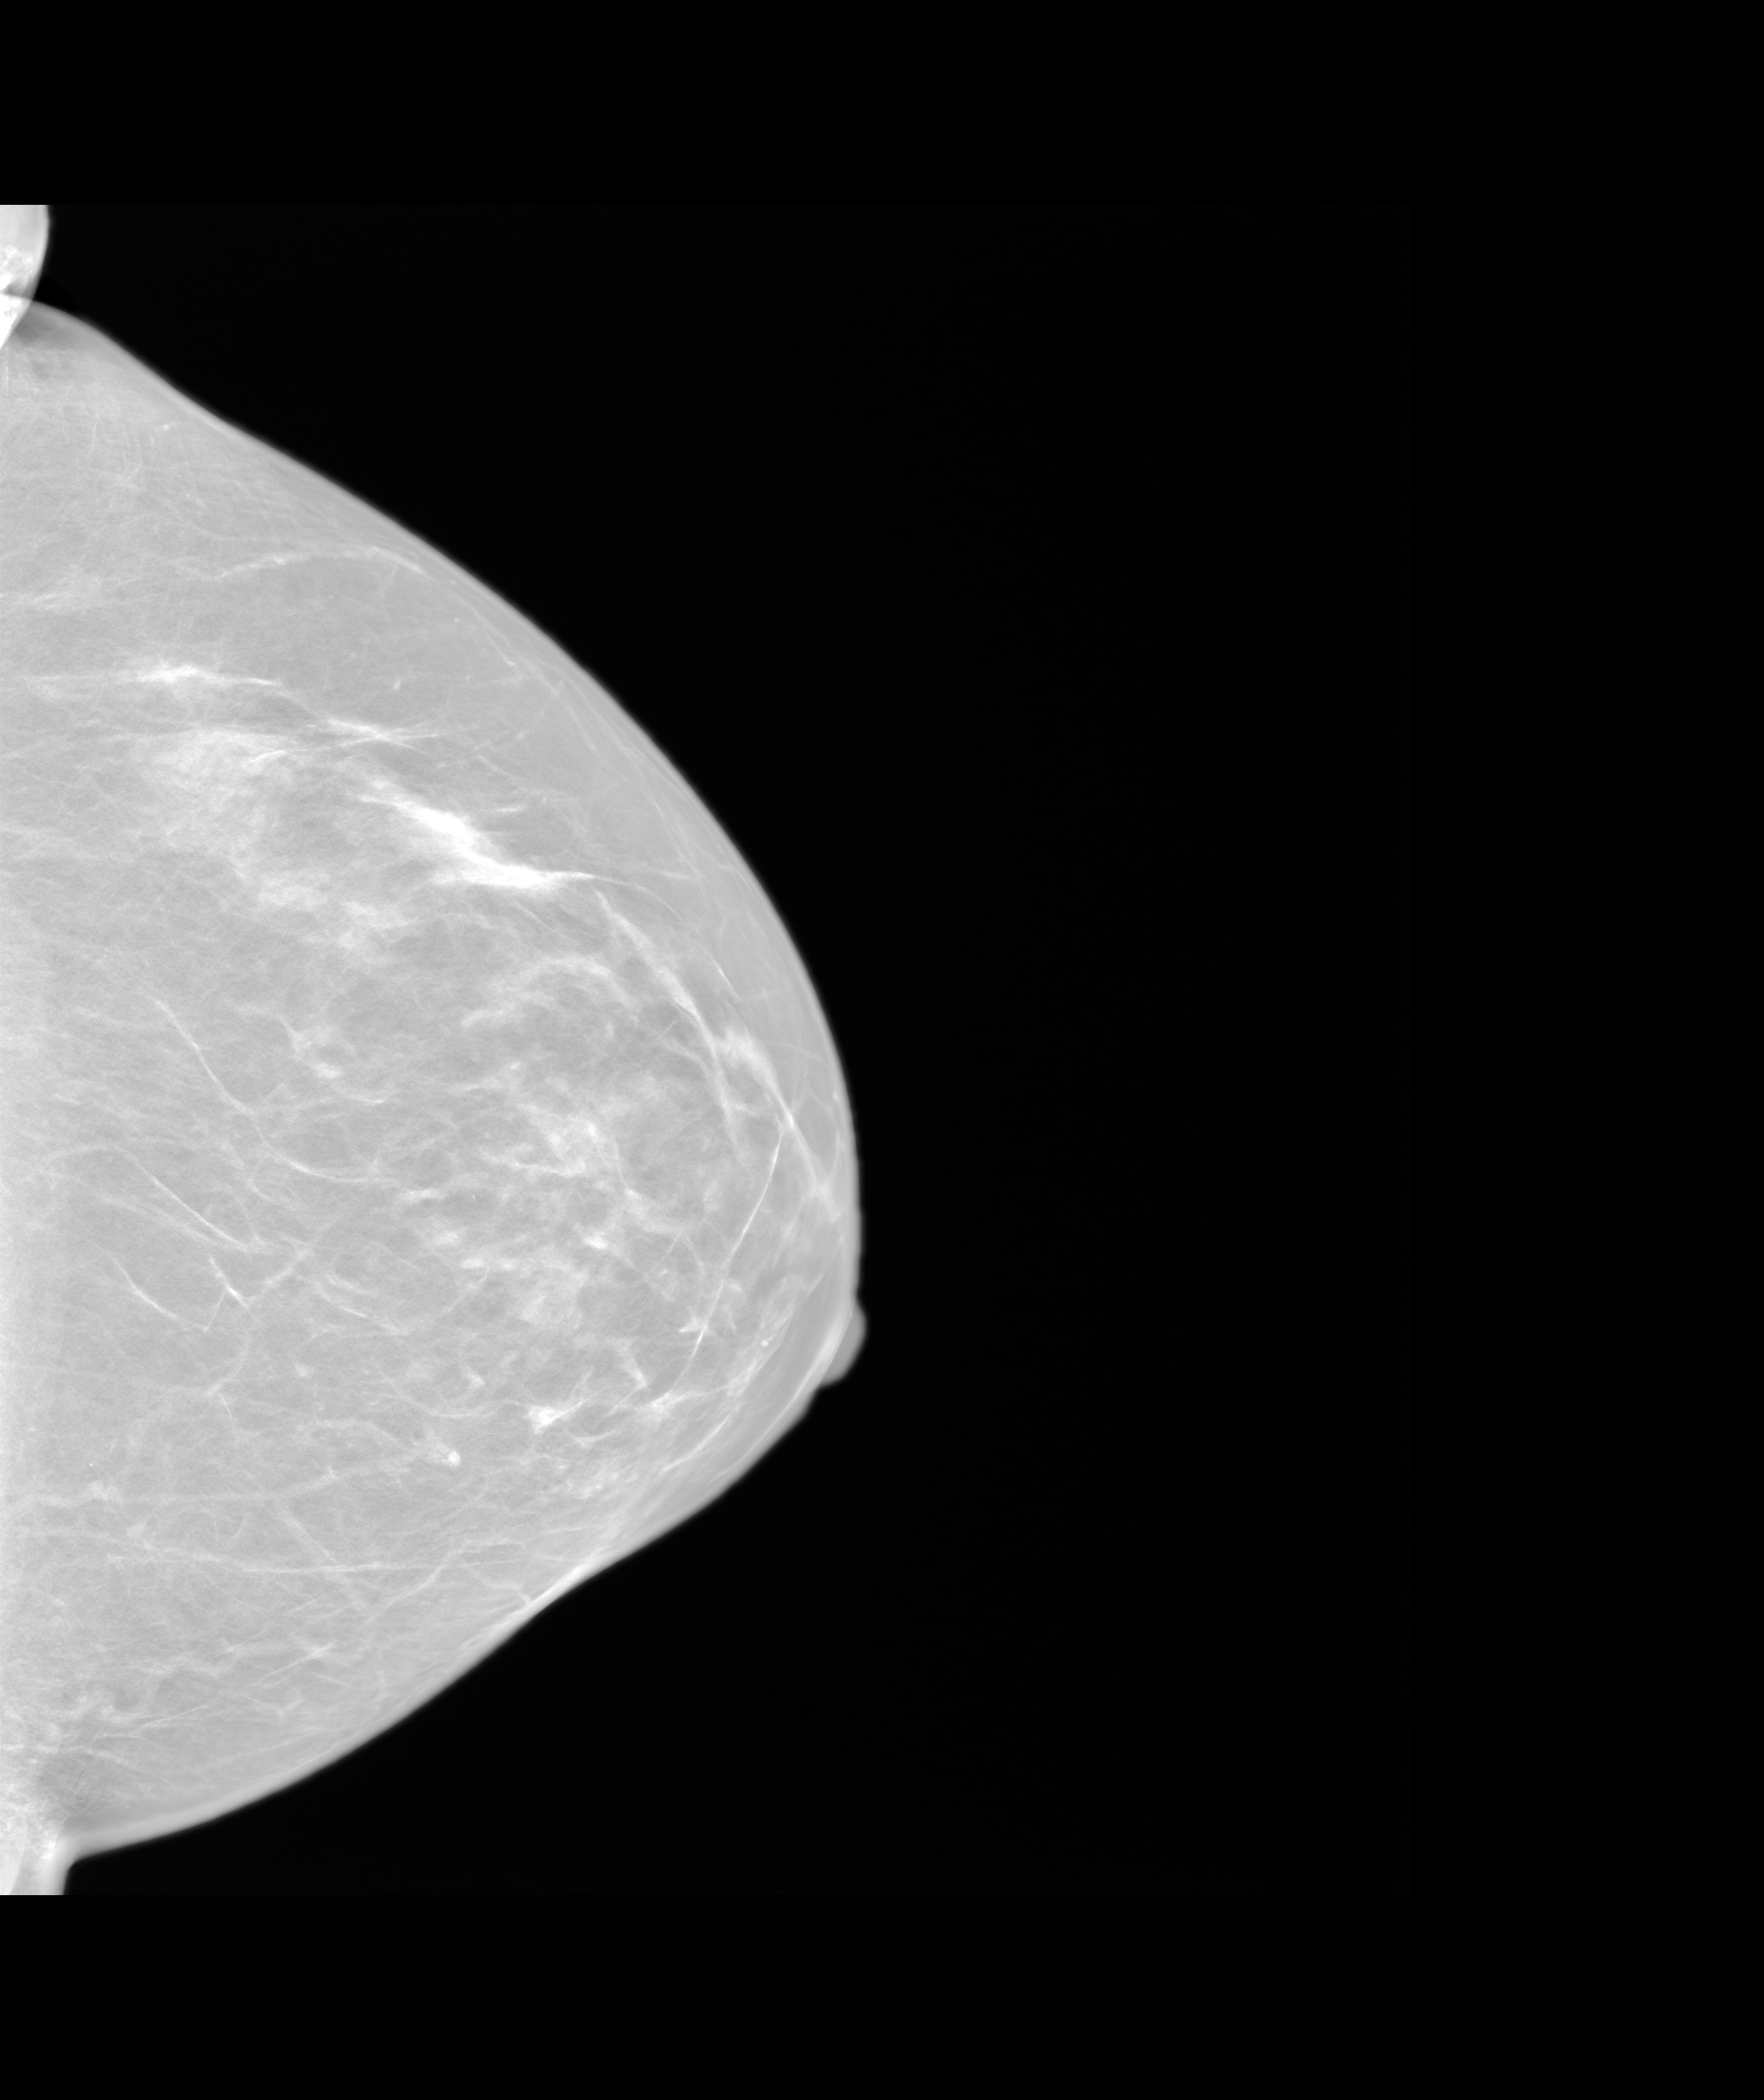
Annual screening mammography examination, system: SenoIris_1SP2(440). Patient aged 58 years (female).
Image type: synthesized 2-D view from tomosynthesis. Breast: left. Projection: craniocaudal (CC) view.